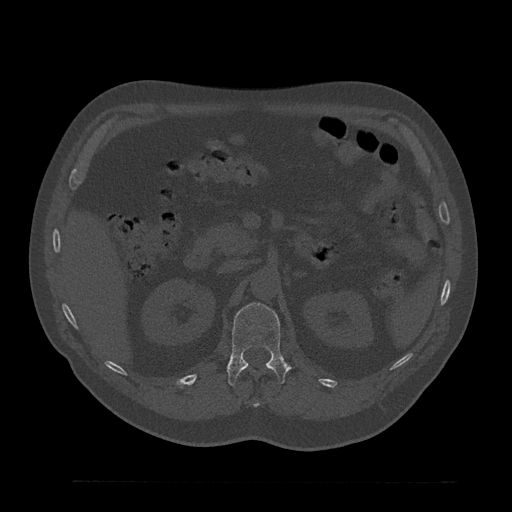
CT including the spine, one axial slice. Reconstruction kernel Br40s/3. Bone window (W 1800 / L 400 HU). 512 × 512 image matrix. Patient: male, 61 years. From the clinical record (not read from this slice): primary cancer: prostate.
Annotated regions visible in this slice (semi-automatic segmentation, software-assisted and operator-edited):
- L1 vertebra: bounding box <227,303,290,386> (left, top, right, bottom; pixels)
- T12 vertebra: <254,403,260,407>